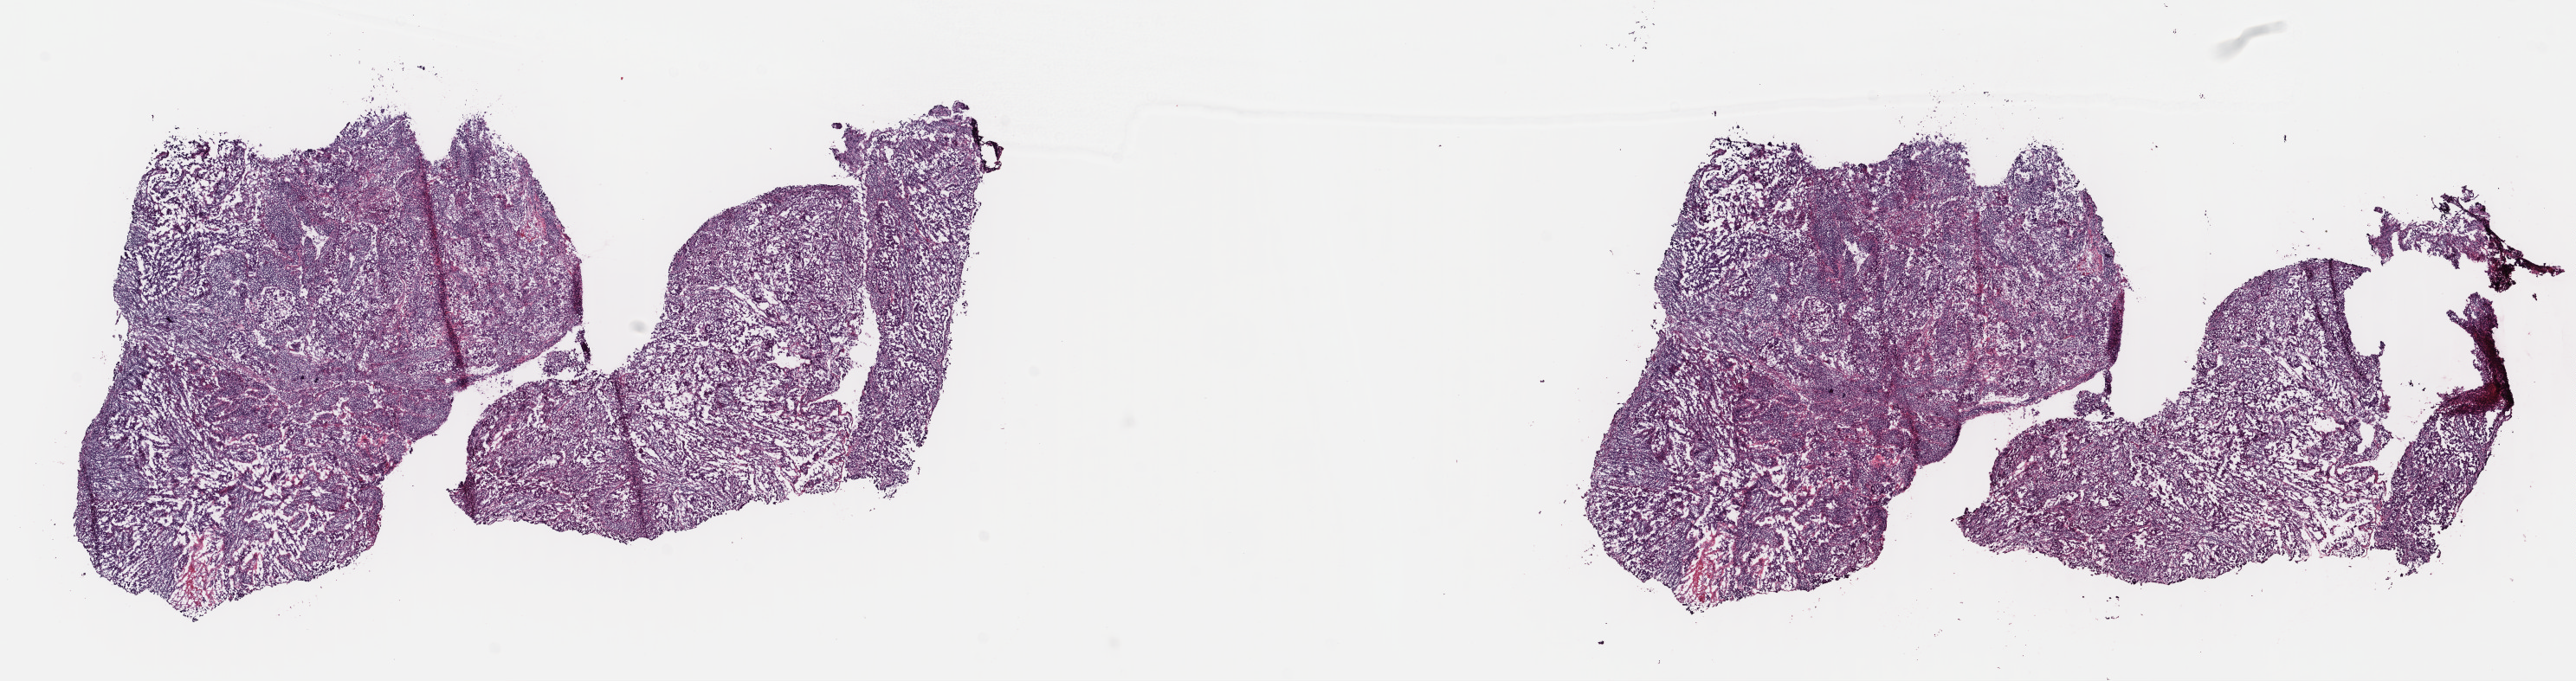
Whole-slide histology image, Hematoxylin and eosin (H&E) stained, shown as a low-resolution overview of the whole scanned area (about 23.4 x 6.2 mm, from a 40x scan), frozen section from the top of the tissue portion, uterus, primary tumour sample. Female, age 68 years at initial diagnosis. Histologic grade: G3 (poorly differentiated). Composition of this section per pathologist review: tumour cells 90%, tumour nuclei 85%, normal cells 0%, stromal cells 5%, necrosis 5%. Infiltration values recorded for this section: lymphocyte infiltration 3%, monocyte infiltration 1%, neutrophil infiltration 0%.
- FIGO stage: IA
- diagnosis: Serous cystadenocarcinoma, NOS (endometrium)